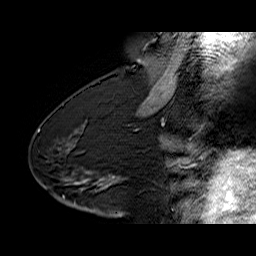
Breast MRI (dynamic contrast-enhanced), one sagittal slice; position 35 of 60 along the scan axis; dynamic contrast-enhanced series, time point 2 of 6 at this slice position (early post-contrast); 1.5 T; TE 6.4 ms, TR 32.9 ms; 4 mm slice thickness; 256 × 256 image matrix, field of view 200 × 200 mm. Female patient. From the clinical record (not read from this slice): setting: breast cancer imaged before/during neoadjuvant chemotherapy; receptor status: HR-positive, HER2-negative.
Annotated regions visible in this slice (semi-automatic segmentation, software-assisted and operator-edited):
- analysis volume of interest (the breast-tissue region the enhancement analysis was run in; not a lesion): bounding box [x1, y1, x2, y2] px = [68, 154, 128, 203]
- tumour enhancement mask (voxels above the 100 % enhancement threshold inside the analysis volume of interest): [99, 176, 114, 189]